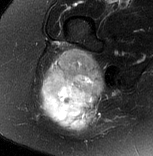
MRI of an extremity soft-tissue mass, one axial slice; slice 49 of 77 in the series (ordered by position); T2-weighted fat-saturated; MR volume resampled by the dataset authors to the PET/CT grid (not the native acquisition matrix); 3.27 mm slice thickness; 153 × 156 image matrix, field of view 149 × 152 mm. Female patient. Case-level facts recorded for this patient, not image findings: histological type: synovial sarcoma; grade: intermediate; site of the primary tumour: right buttock.
Outlined on this slice (expert contour drawn on MRI and transferred to this co-registered scan by the dataset authors):
- gross tumour volume including surrounding oedema: box from (x=42, y=49) to (x=104, y=132) px
- gross tumour volume (mass): (x=42, y=49)–(x=104, y=121)